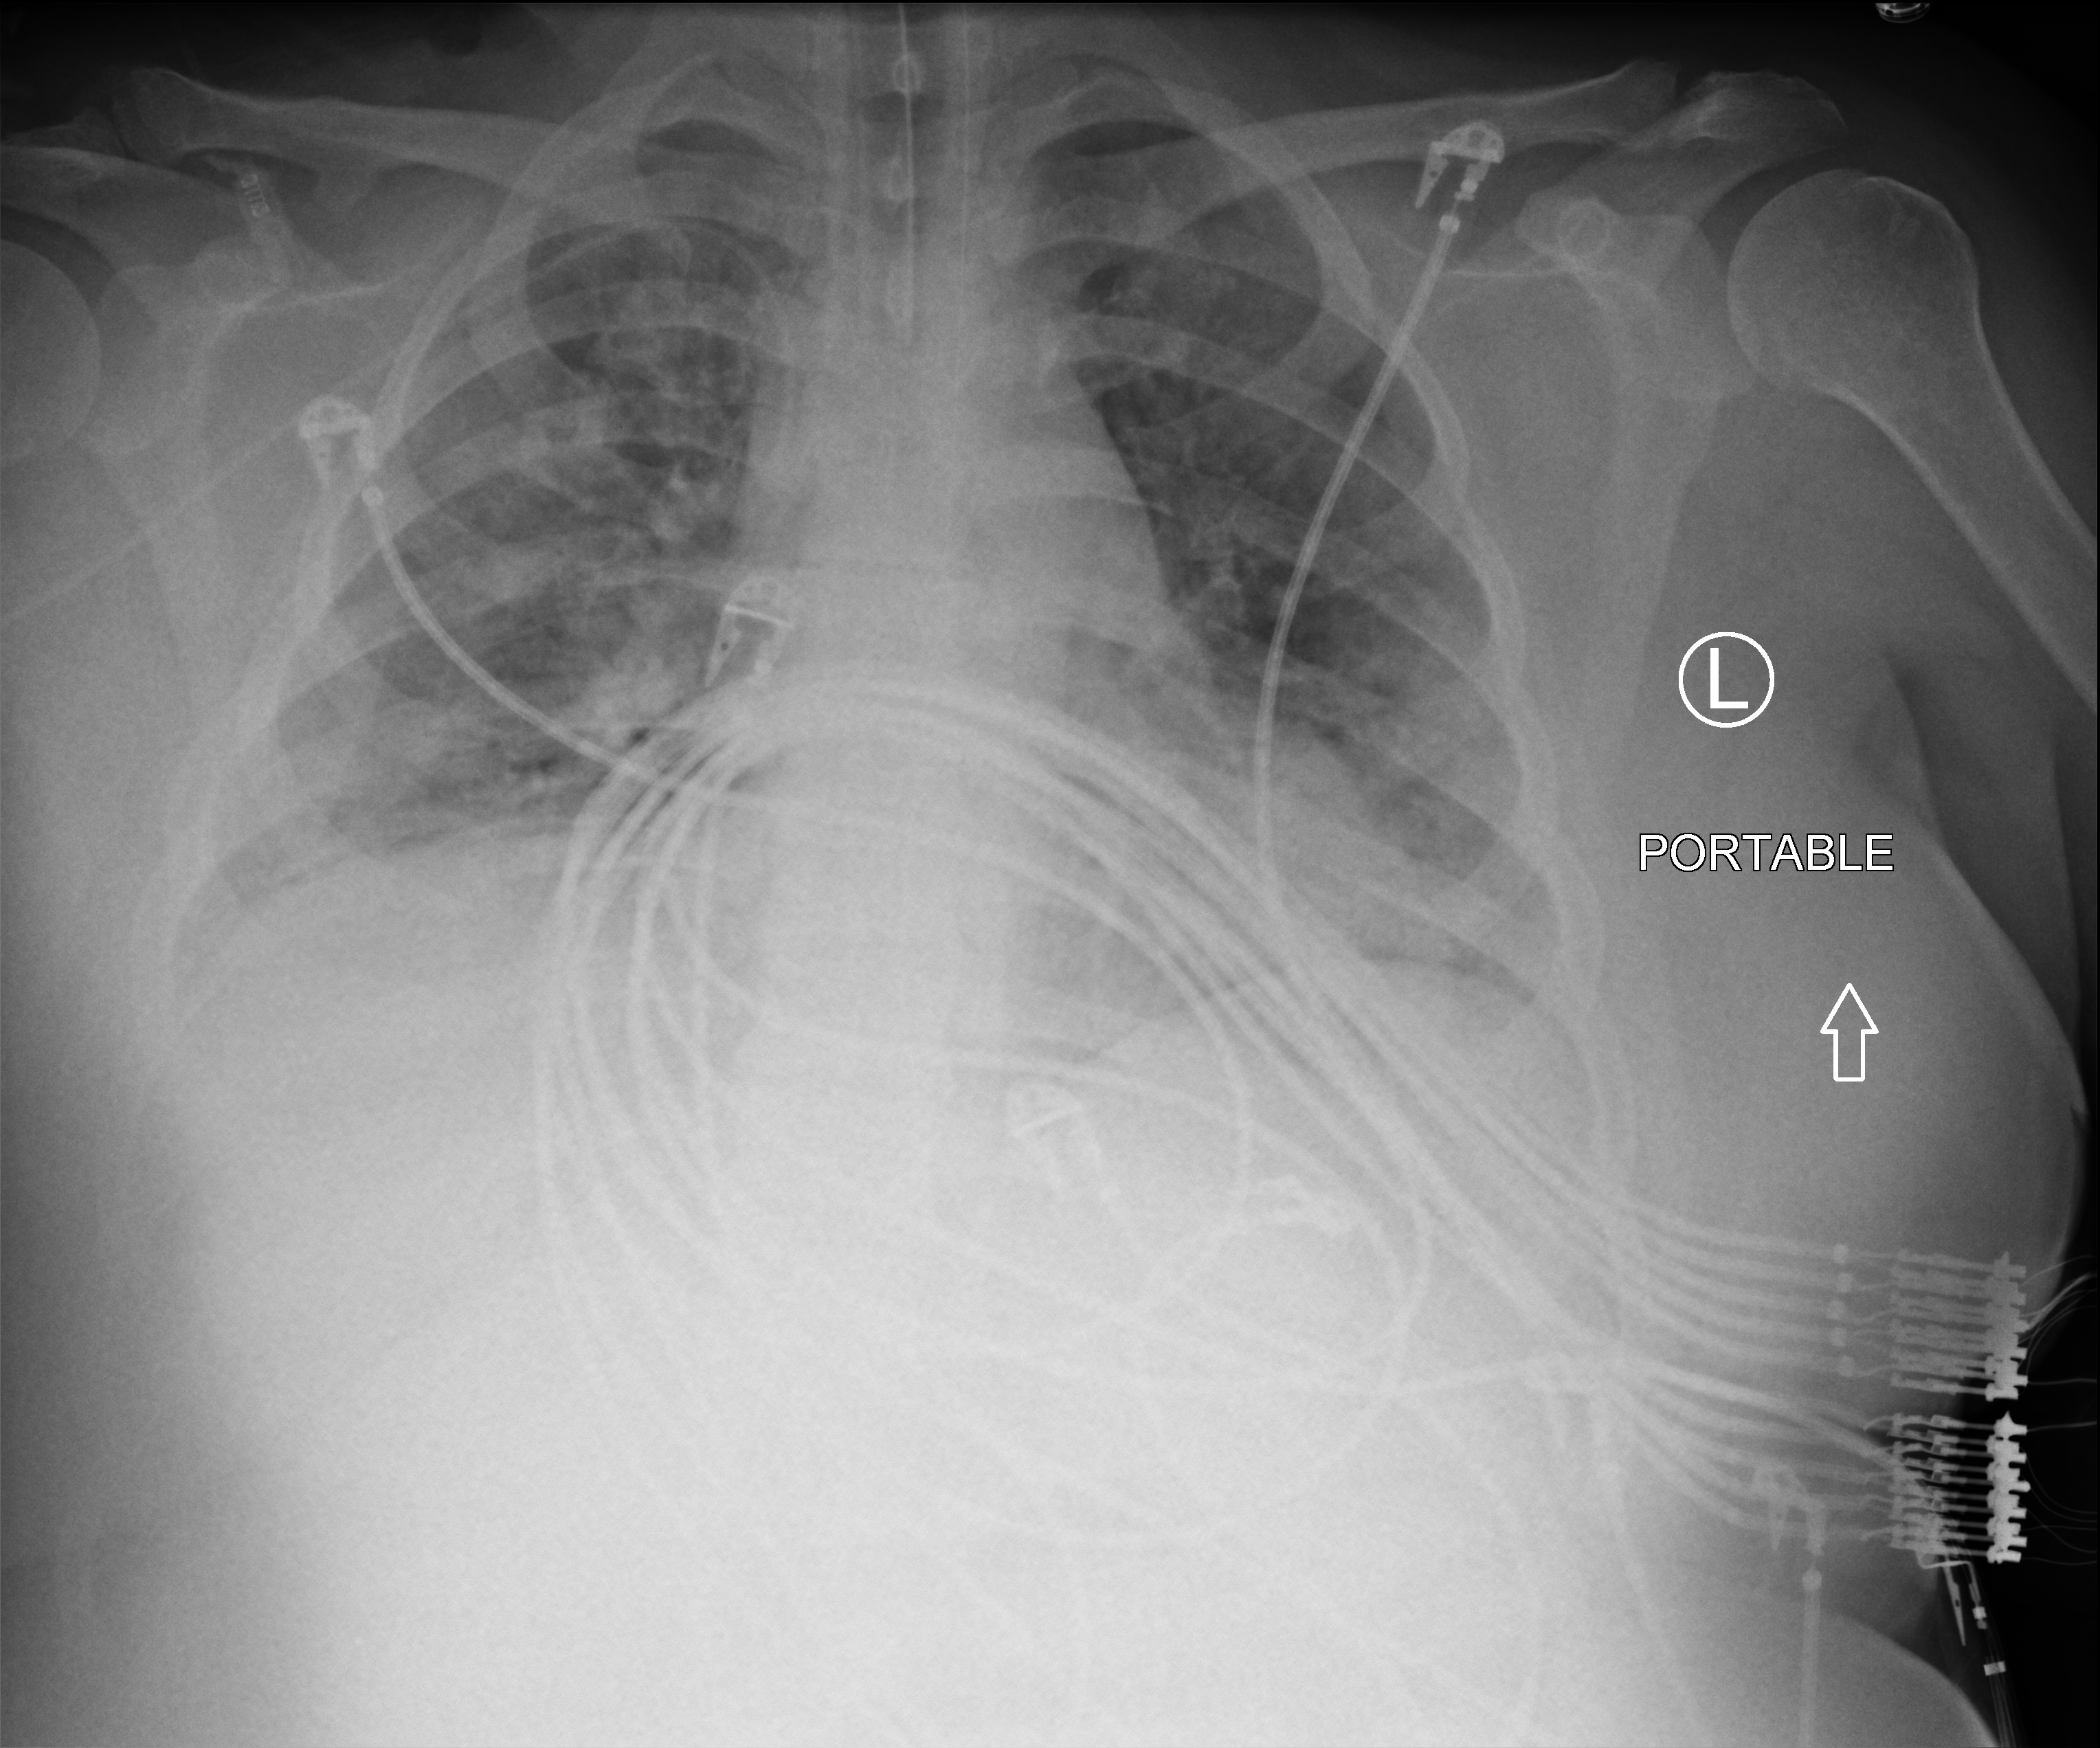
Chest X-ray (portable), anteroposterior (AP) projection. Patient hospitalised with COVID-19; female, aged 18–59 years.
Admission-level facts for this patient (not findings on this image; timing relative to this image not recorded):
- other chronic lung disease (admission record): no